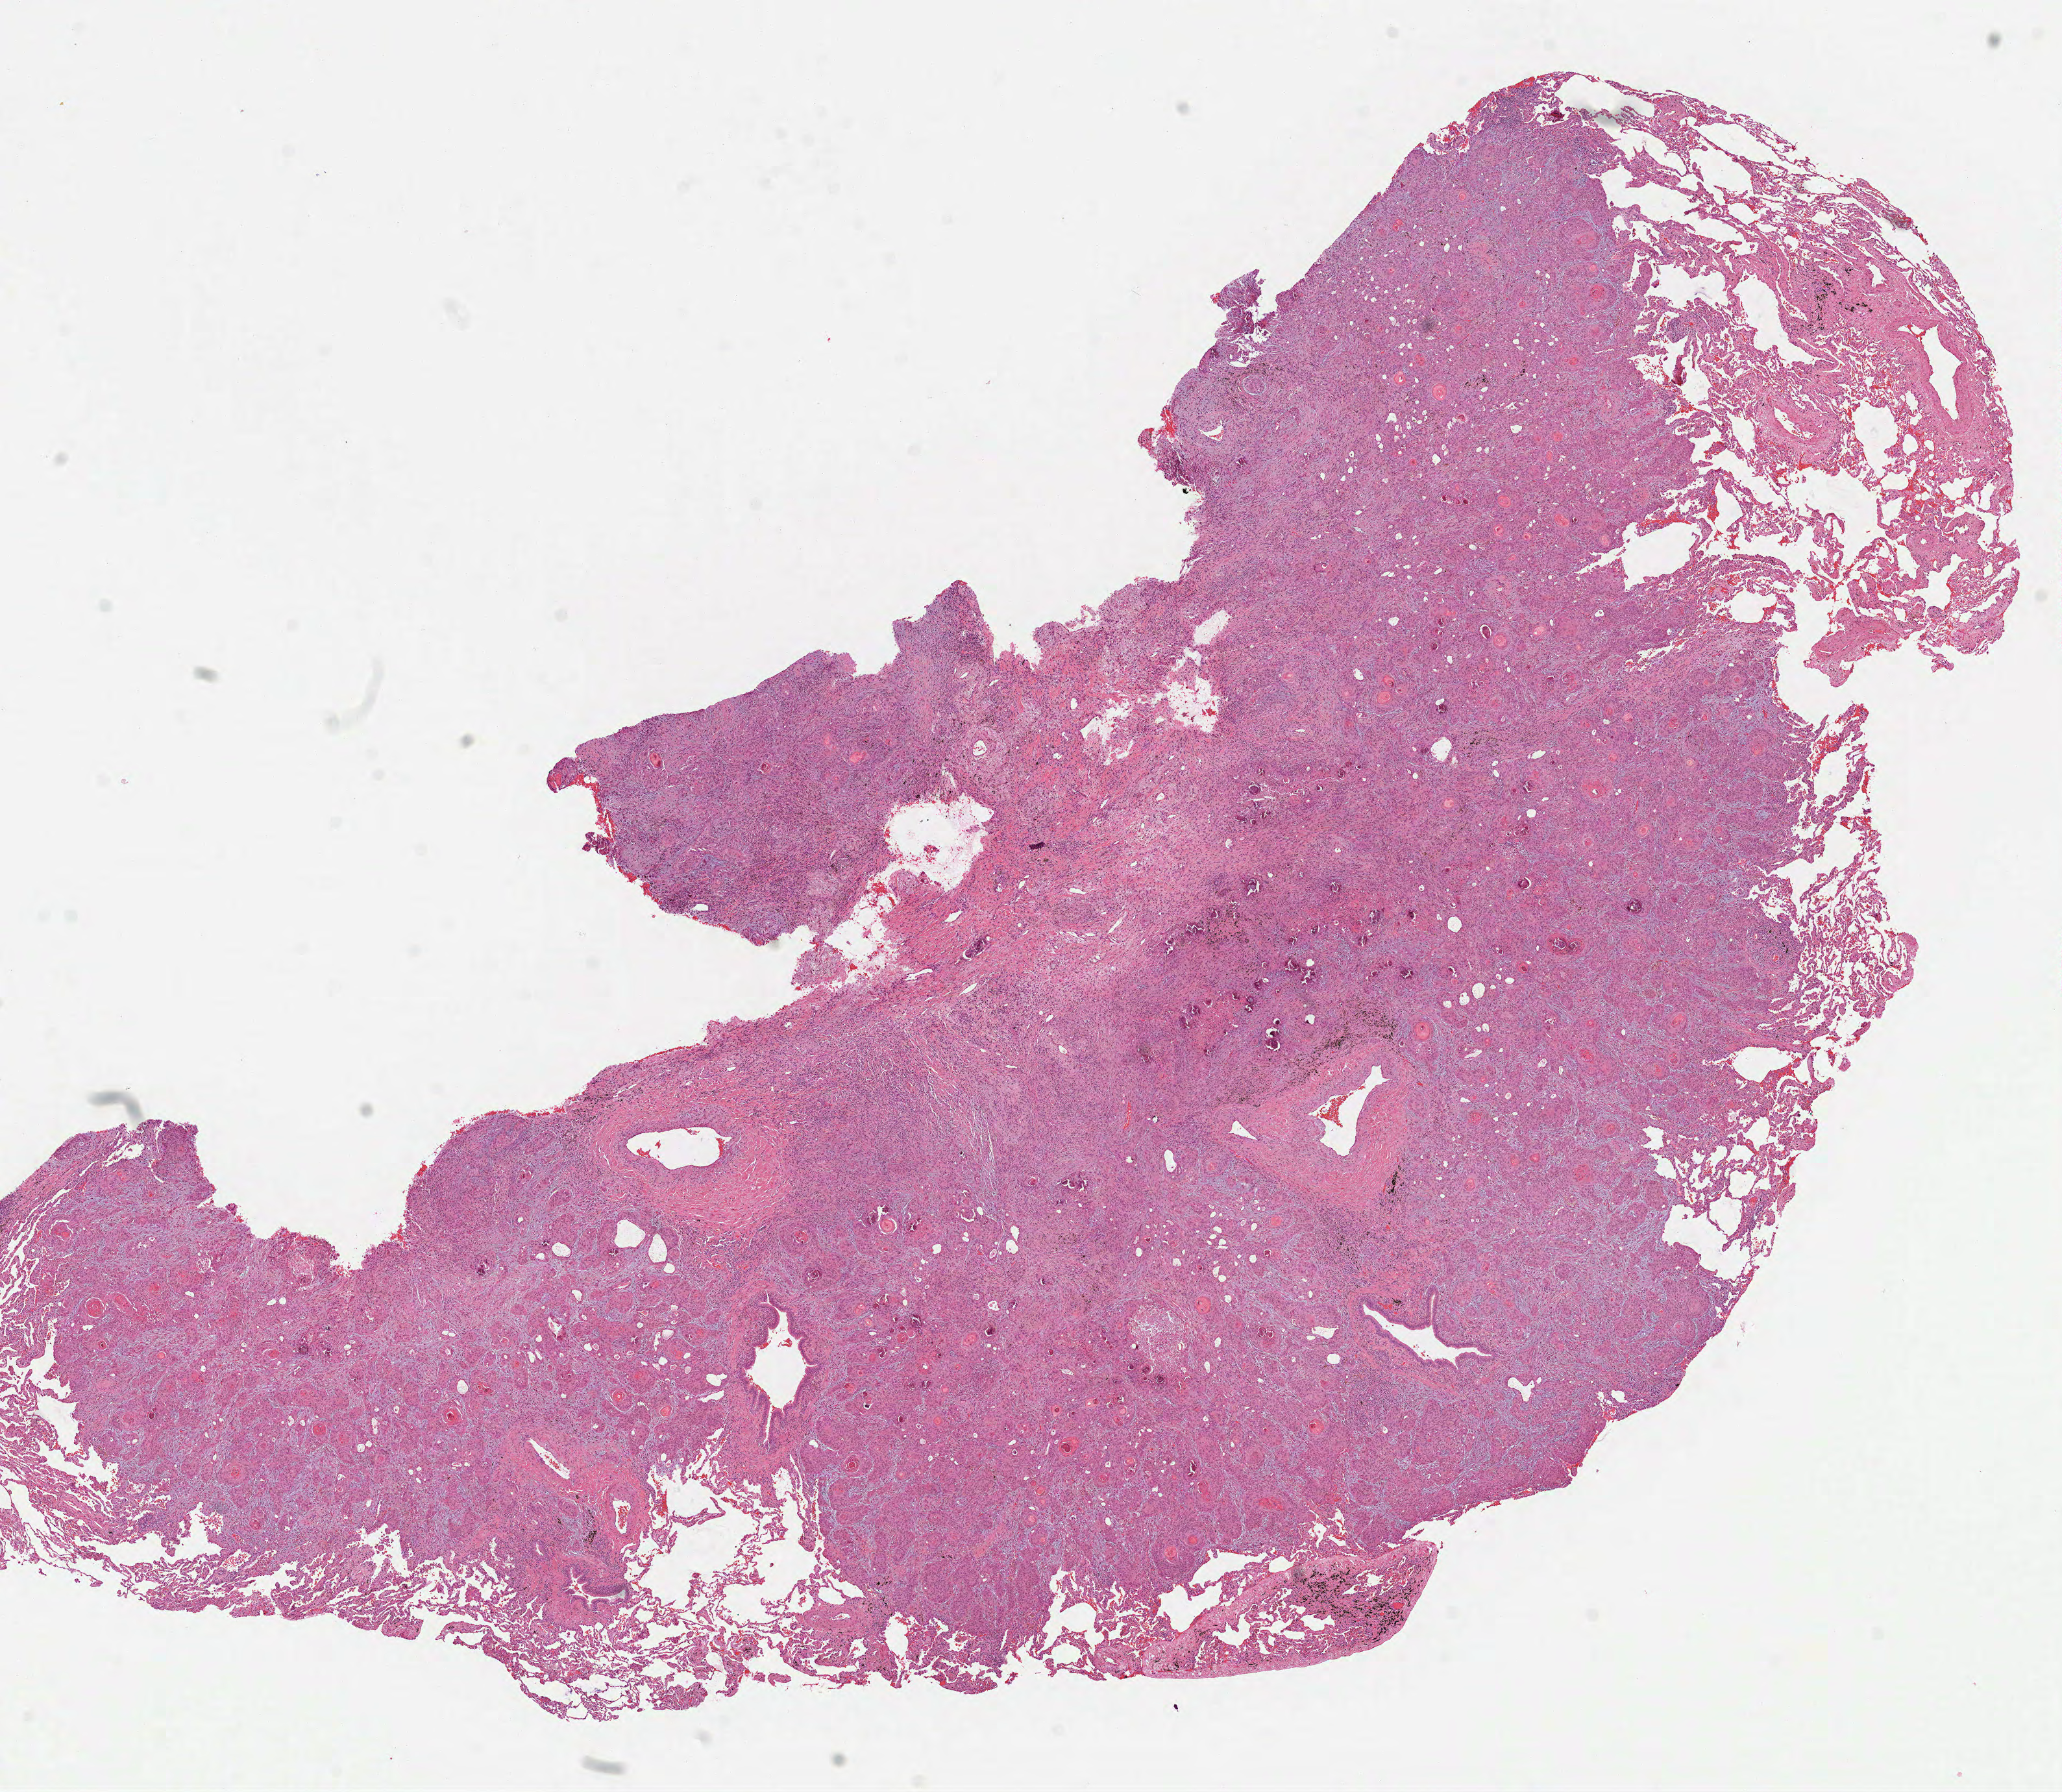
Digitized H&E-stained tissue section (whole slide) — whole scanned area (about 12.8 x 11.1 mm) shown as a low-resolution overview; formalin-fixed paraffin-embedded (FFPE) diagnostic section; lung, primary tumour sample. Male patient; age at initial diagnosis 59 years.
AJCC pathologic stage: IA (7th edition). Pathologic diagnosis: Squamous cell carcinoma, NOS.